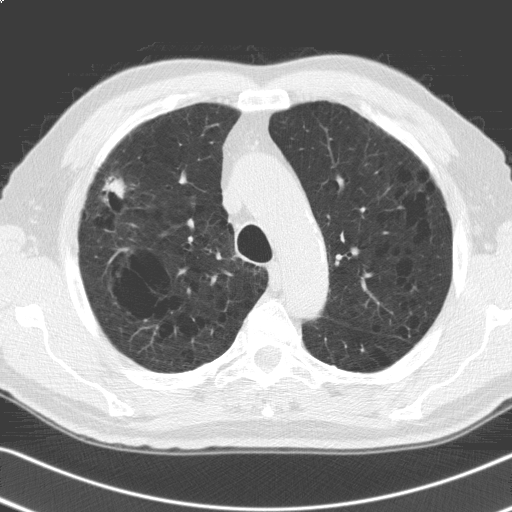
Low-dose screening chest CT, axial slice; second annual screen; lung window (W 1500 / L -600 HU); standard (soft-tissue) reconstruction kernel (C); slice 41 of 168 in the series; 512 × 512 image matrix. Male, age 69 years at enrolment. Former smoker at enrolment.
Lesion marked by an expert reader, bounding box (x1, y1, x2, y2) in pixels: (86, 167, 131, 214). The screening reader recorded 6 non-calcified nodules or masses ≥4 mm on this exam (right upper lobe, right upper lobe, right lower lobe, lingula, left lower lobe, left lower lobe); which of them this box marks is not recorded. Official screen result: positive, other. Participant outcome: lung cancer diagnosed 91 days after this screen — adenosquamous carcinoma, right upper lobe, poorly differentiated (G3), stage IV (AJCC 6th edition), 30 mm at pathology.